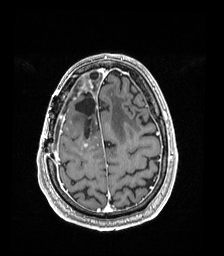
Brain MRI from a brain-tumour surgery series, one axial slice. Position 46 of 192 along the scan axis. T1-weighted post-contrast. 1 mm slice thickness. 224 × 256 image matrix, field of view 224 × 256 mm. From the clinical record (not read from this slice): histopathology: Astrocytoma; WHO grade: 4; IDH mutation: yes.
Structures marked on this image (outlined manually by an expert reader):
- previous resection cavity: box from (x=75, y=92) to (x=96, y=133) px
- tumour: (x=79, y=83)–(x=88, y=94)